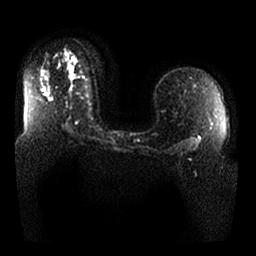
Breast MRI, one axial slice; position 17 of 25 along the scan axis; diffusion-weighted series; image 2 of 4 stored at this slice position (different b-values; order by instance number); 1.5 T; 4 mm slice thickness; 256 × 256 image matrix. Female patient.
Structures marked on this image (outlined manually by an expert reader):
- tumour on diffusion-weighted imaging: bounding box (x1, y1, x2, y2) in pixels: (70, 66, 74, 78)